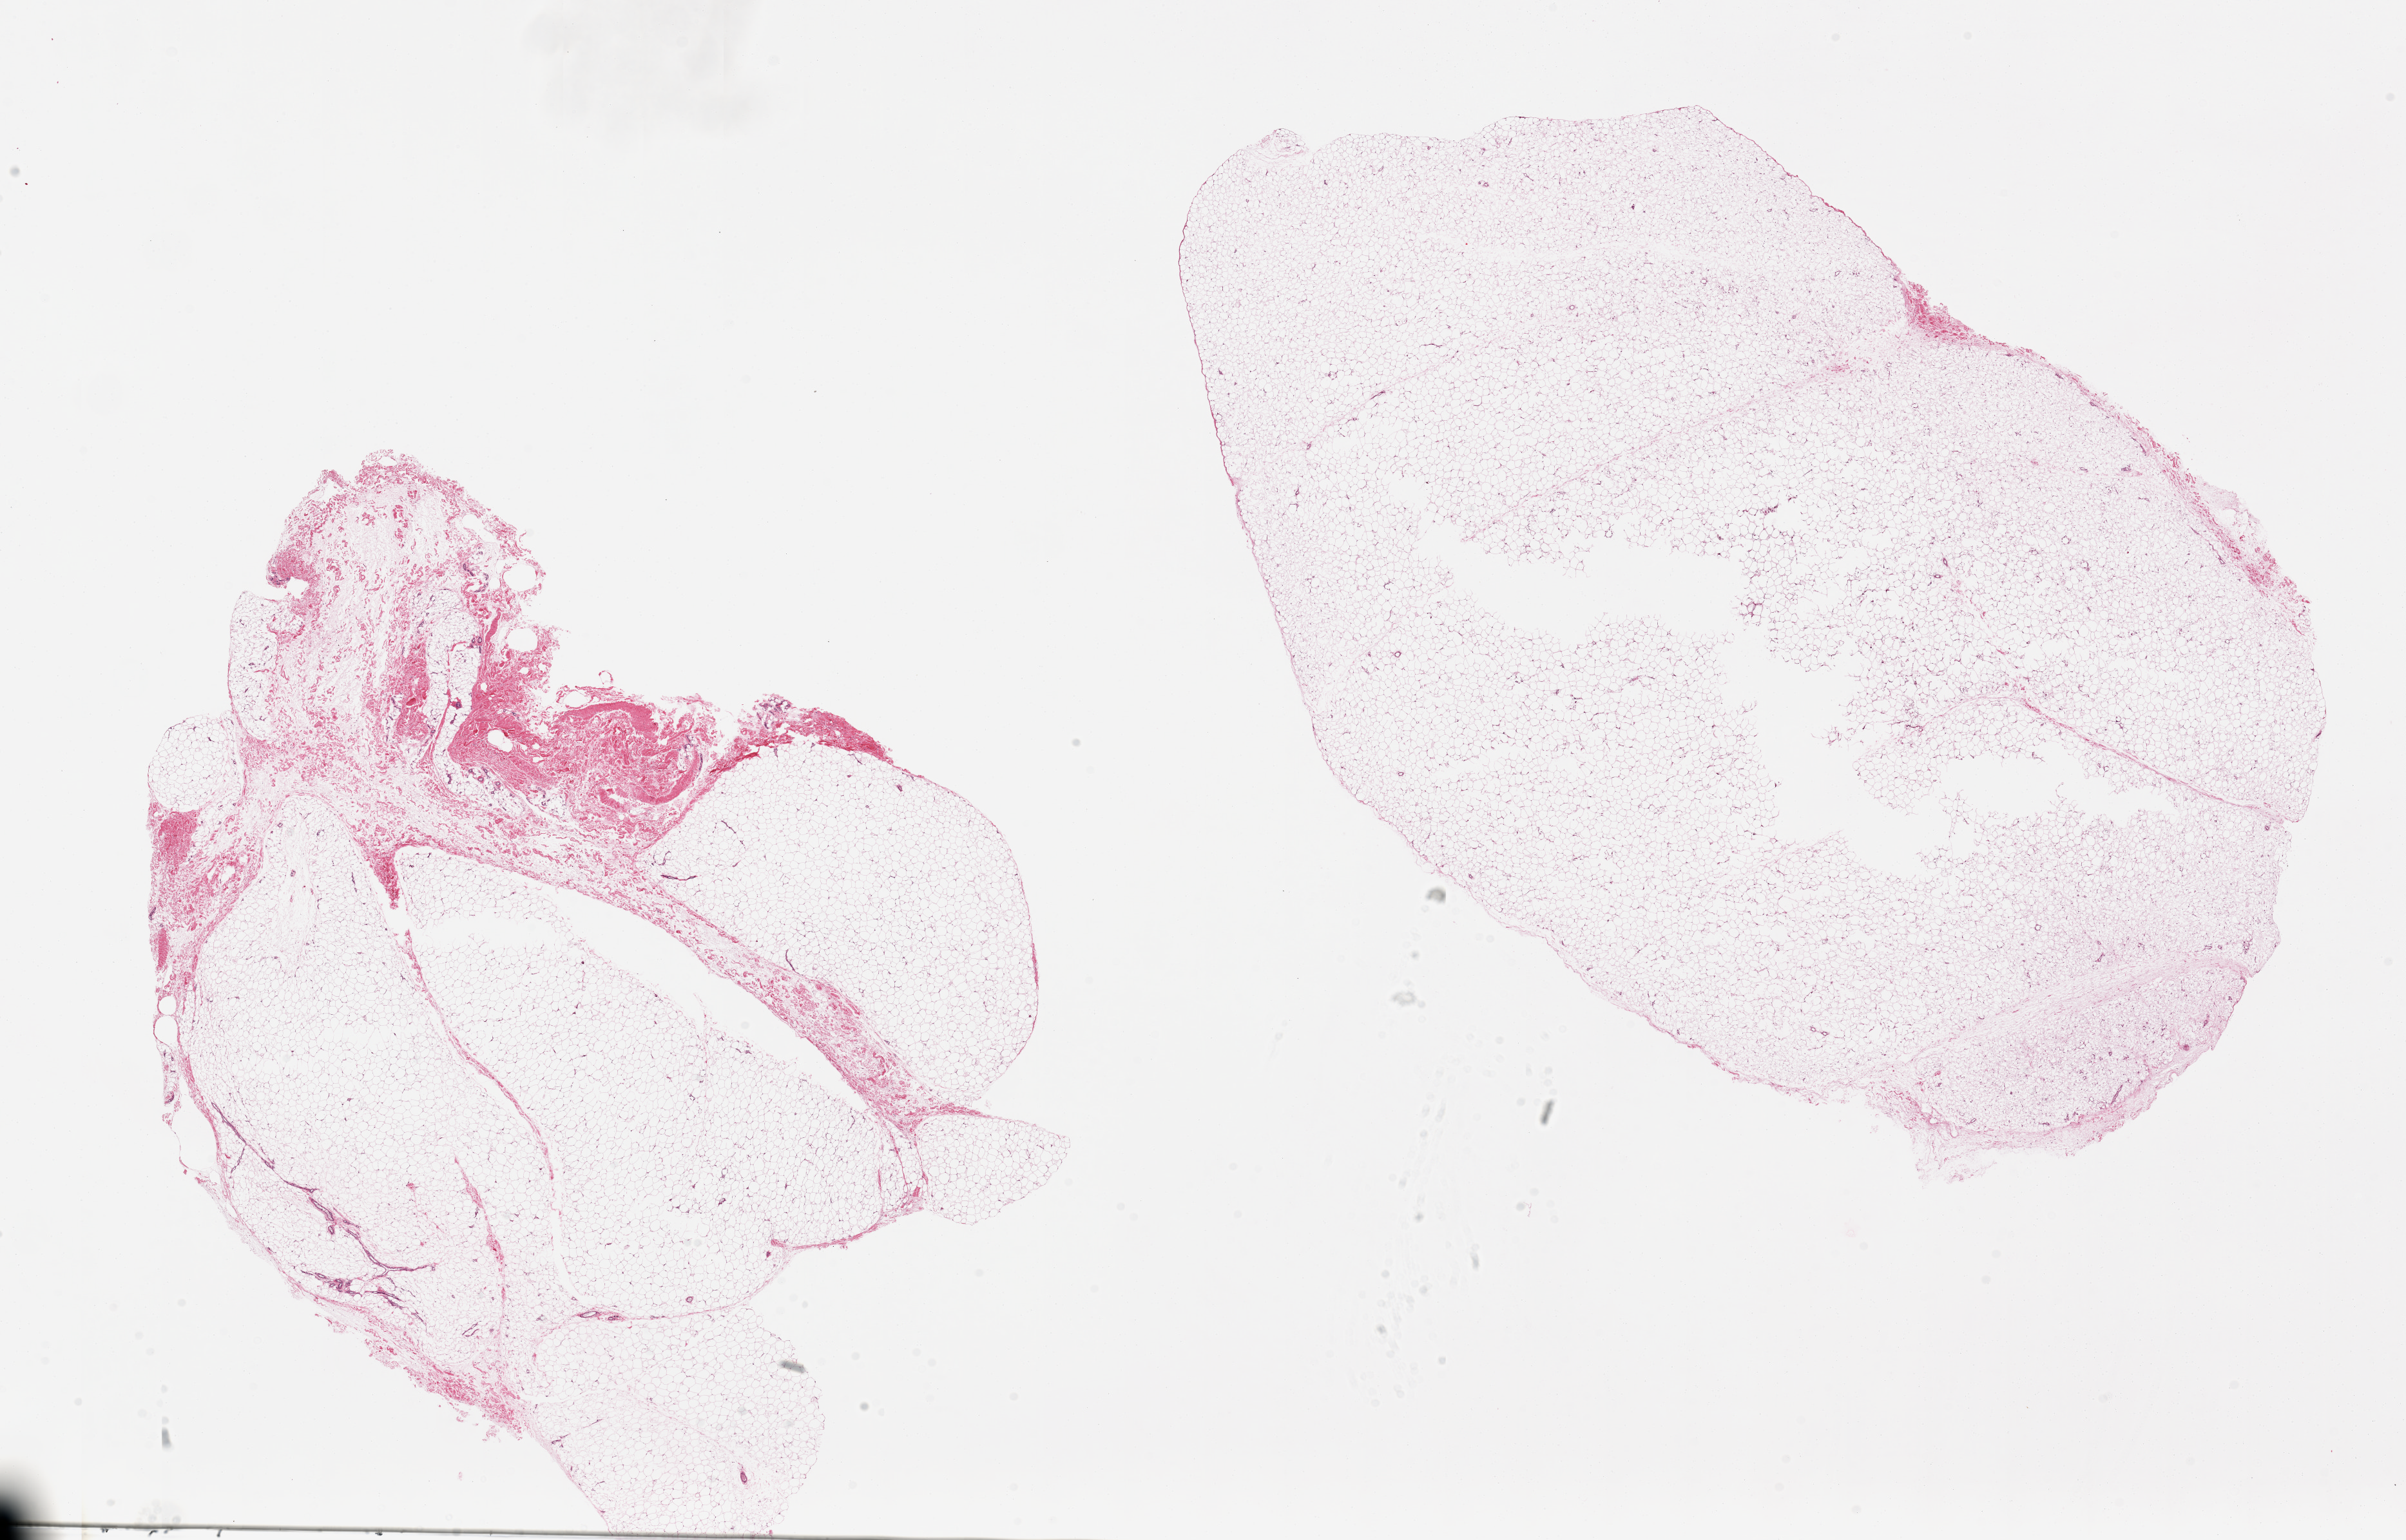
Digitized H&E-stained section, brightfield — low-resolution overview of the scanned area, about 29.5 x 18.9 mm (acquisition: 20x scan); PAXgene-fixed paraffin-embedded (PFPE) section; sampled site (target tissue): adipose tissue; donor tissue sample. Male donor.
• reviewer comment on this tissue sample: 2 pieces. 13x10 & 16x10mm; 10% stroma in 1